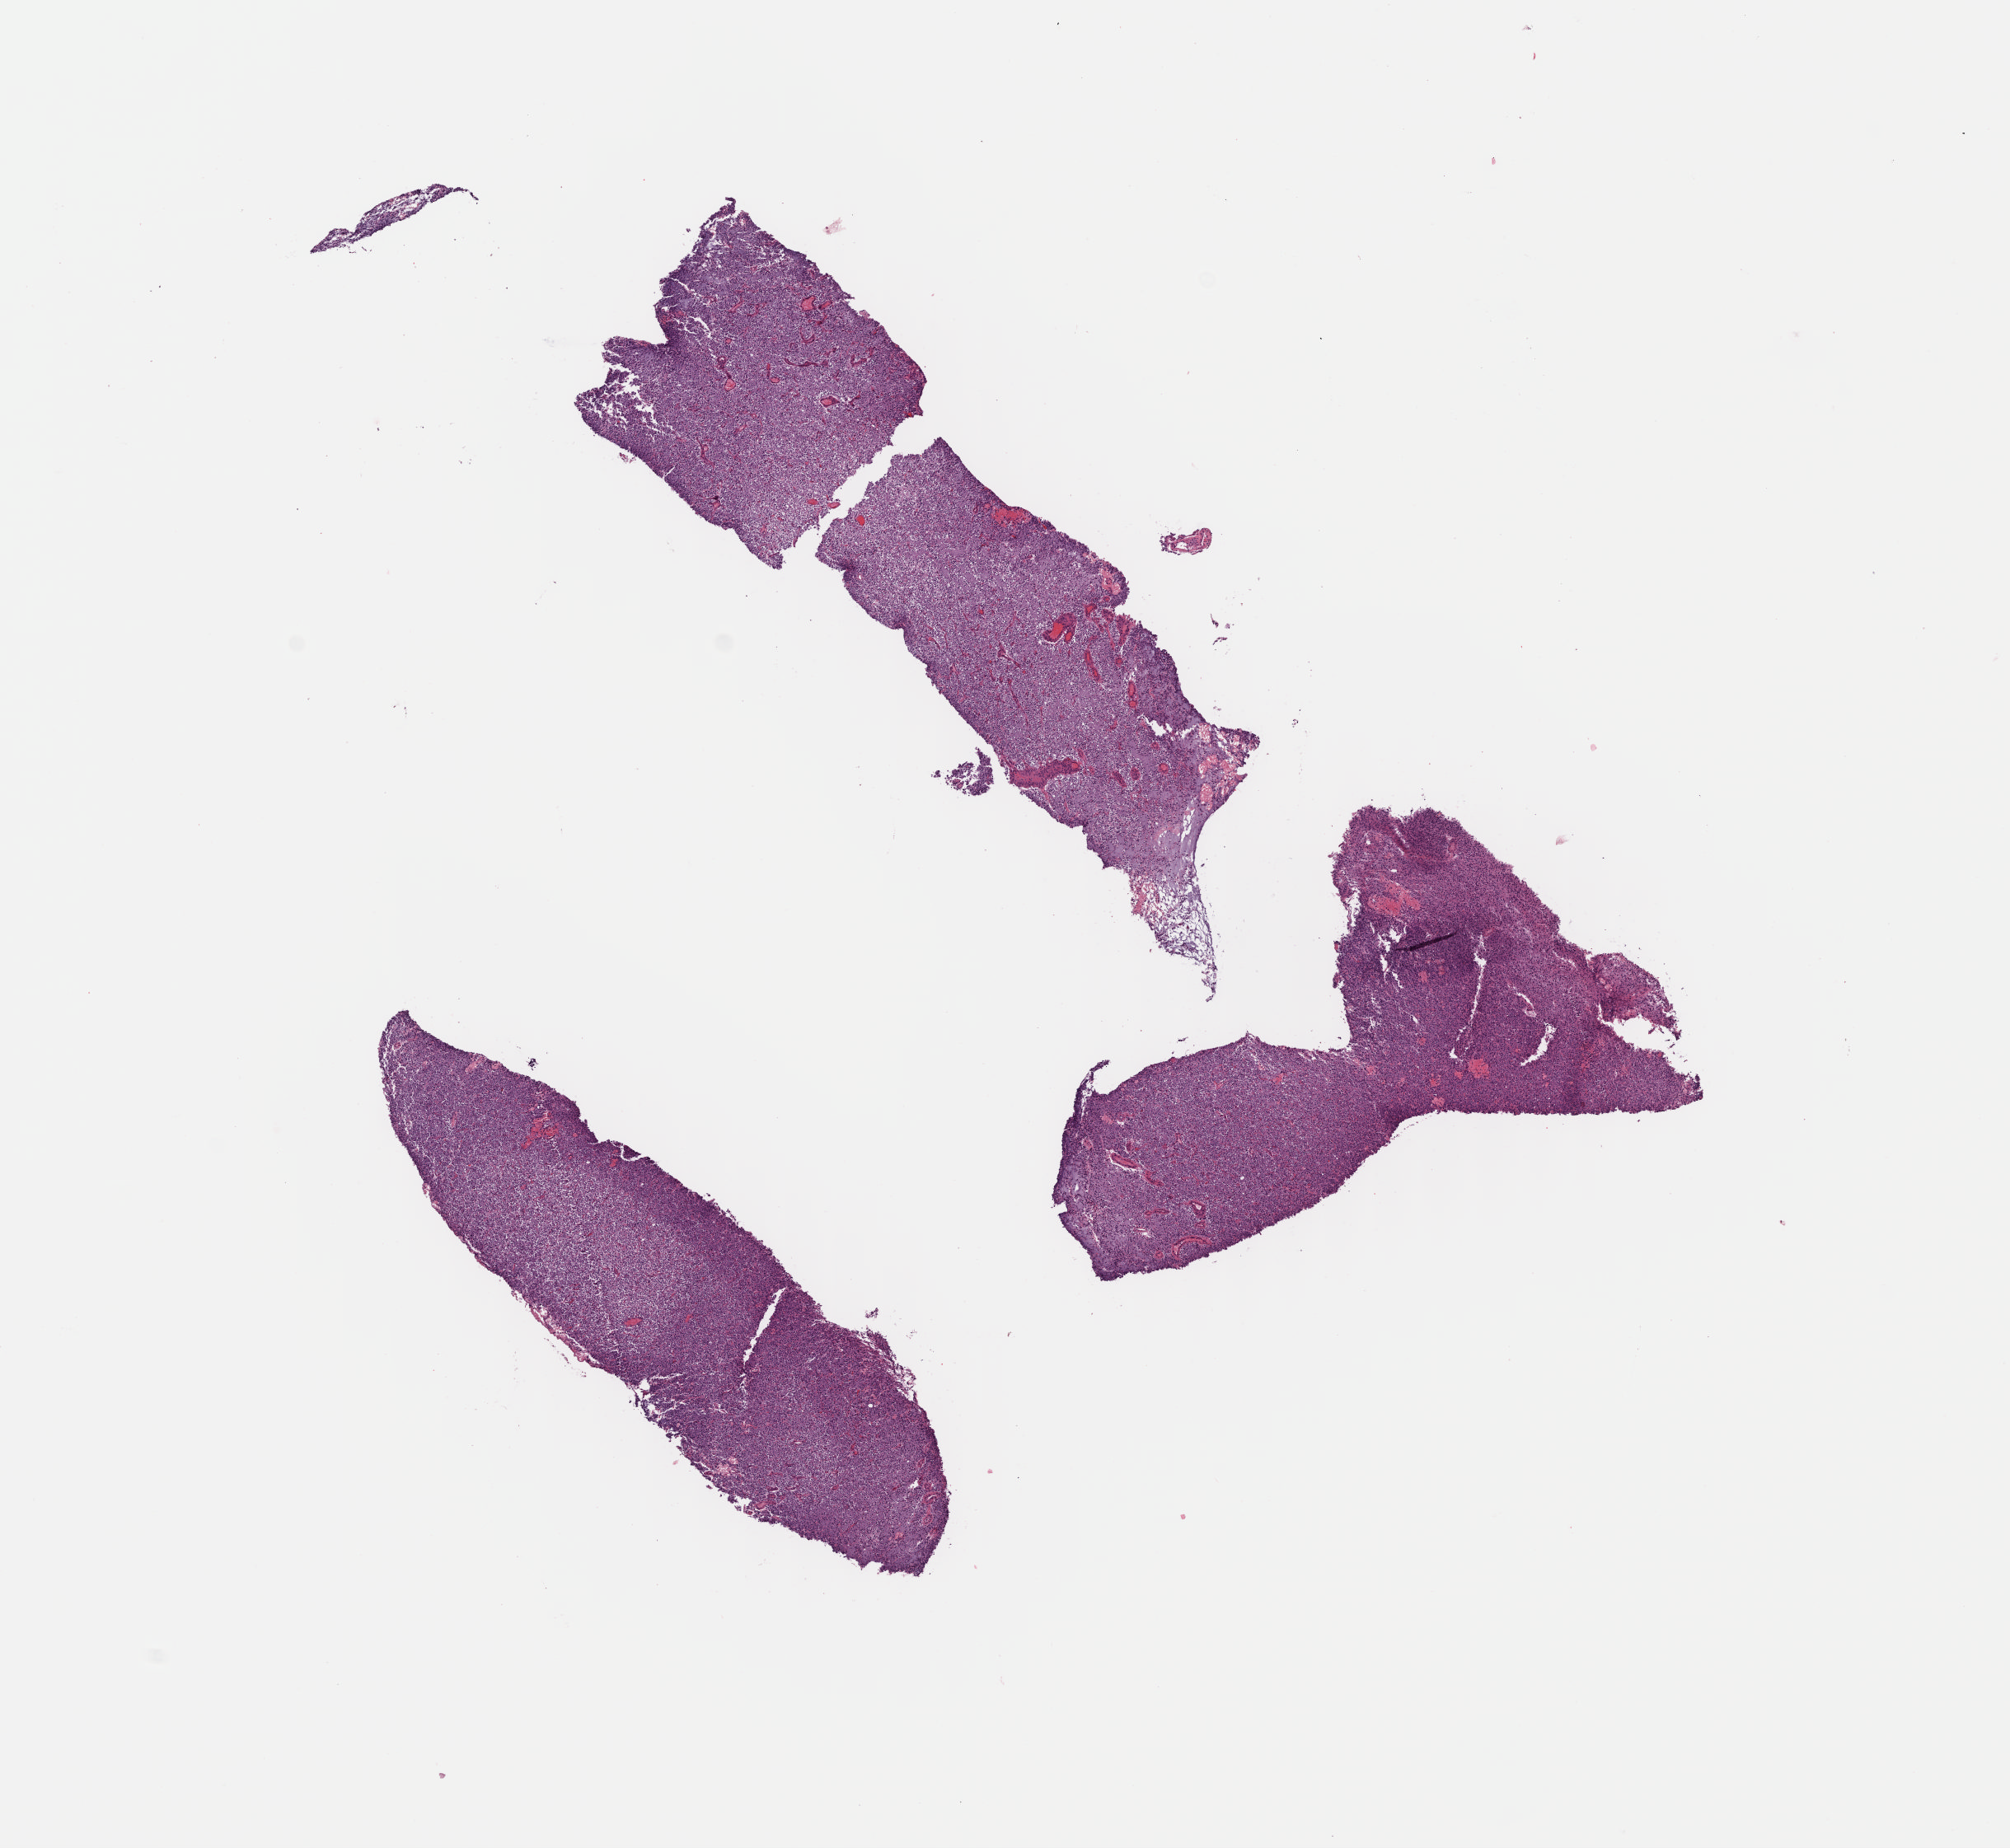
Digitized H&E-stained tissue section (whole slide) — shown as a low-resolution overview of the whole scanned area (about 9.6 x 8.8 mm), formalin-fixed paraffin-embedded (FFPE) diagnostic section, primary tumour sample from the brain. Patient: male, age at initial diagnosis 30 years.
Pathologic diagnosis: Oligodendroglioma, anaplastic (cerebrum).